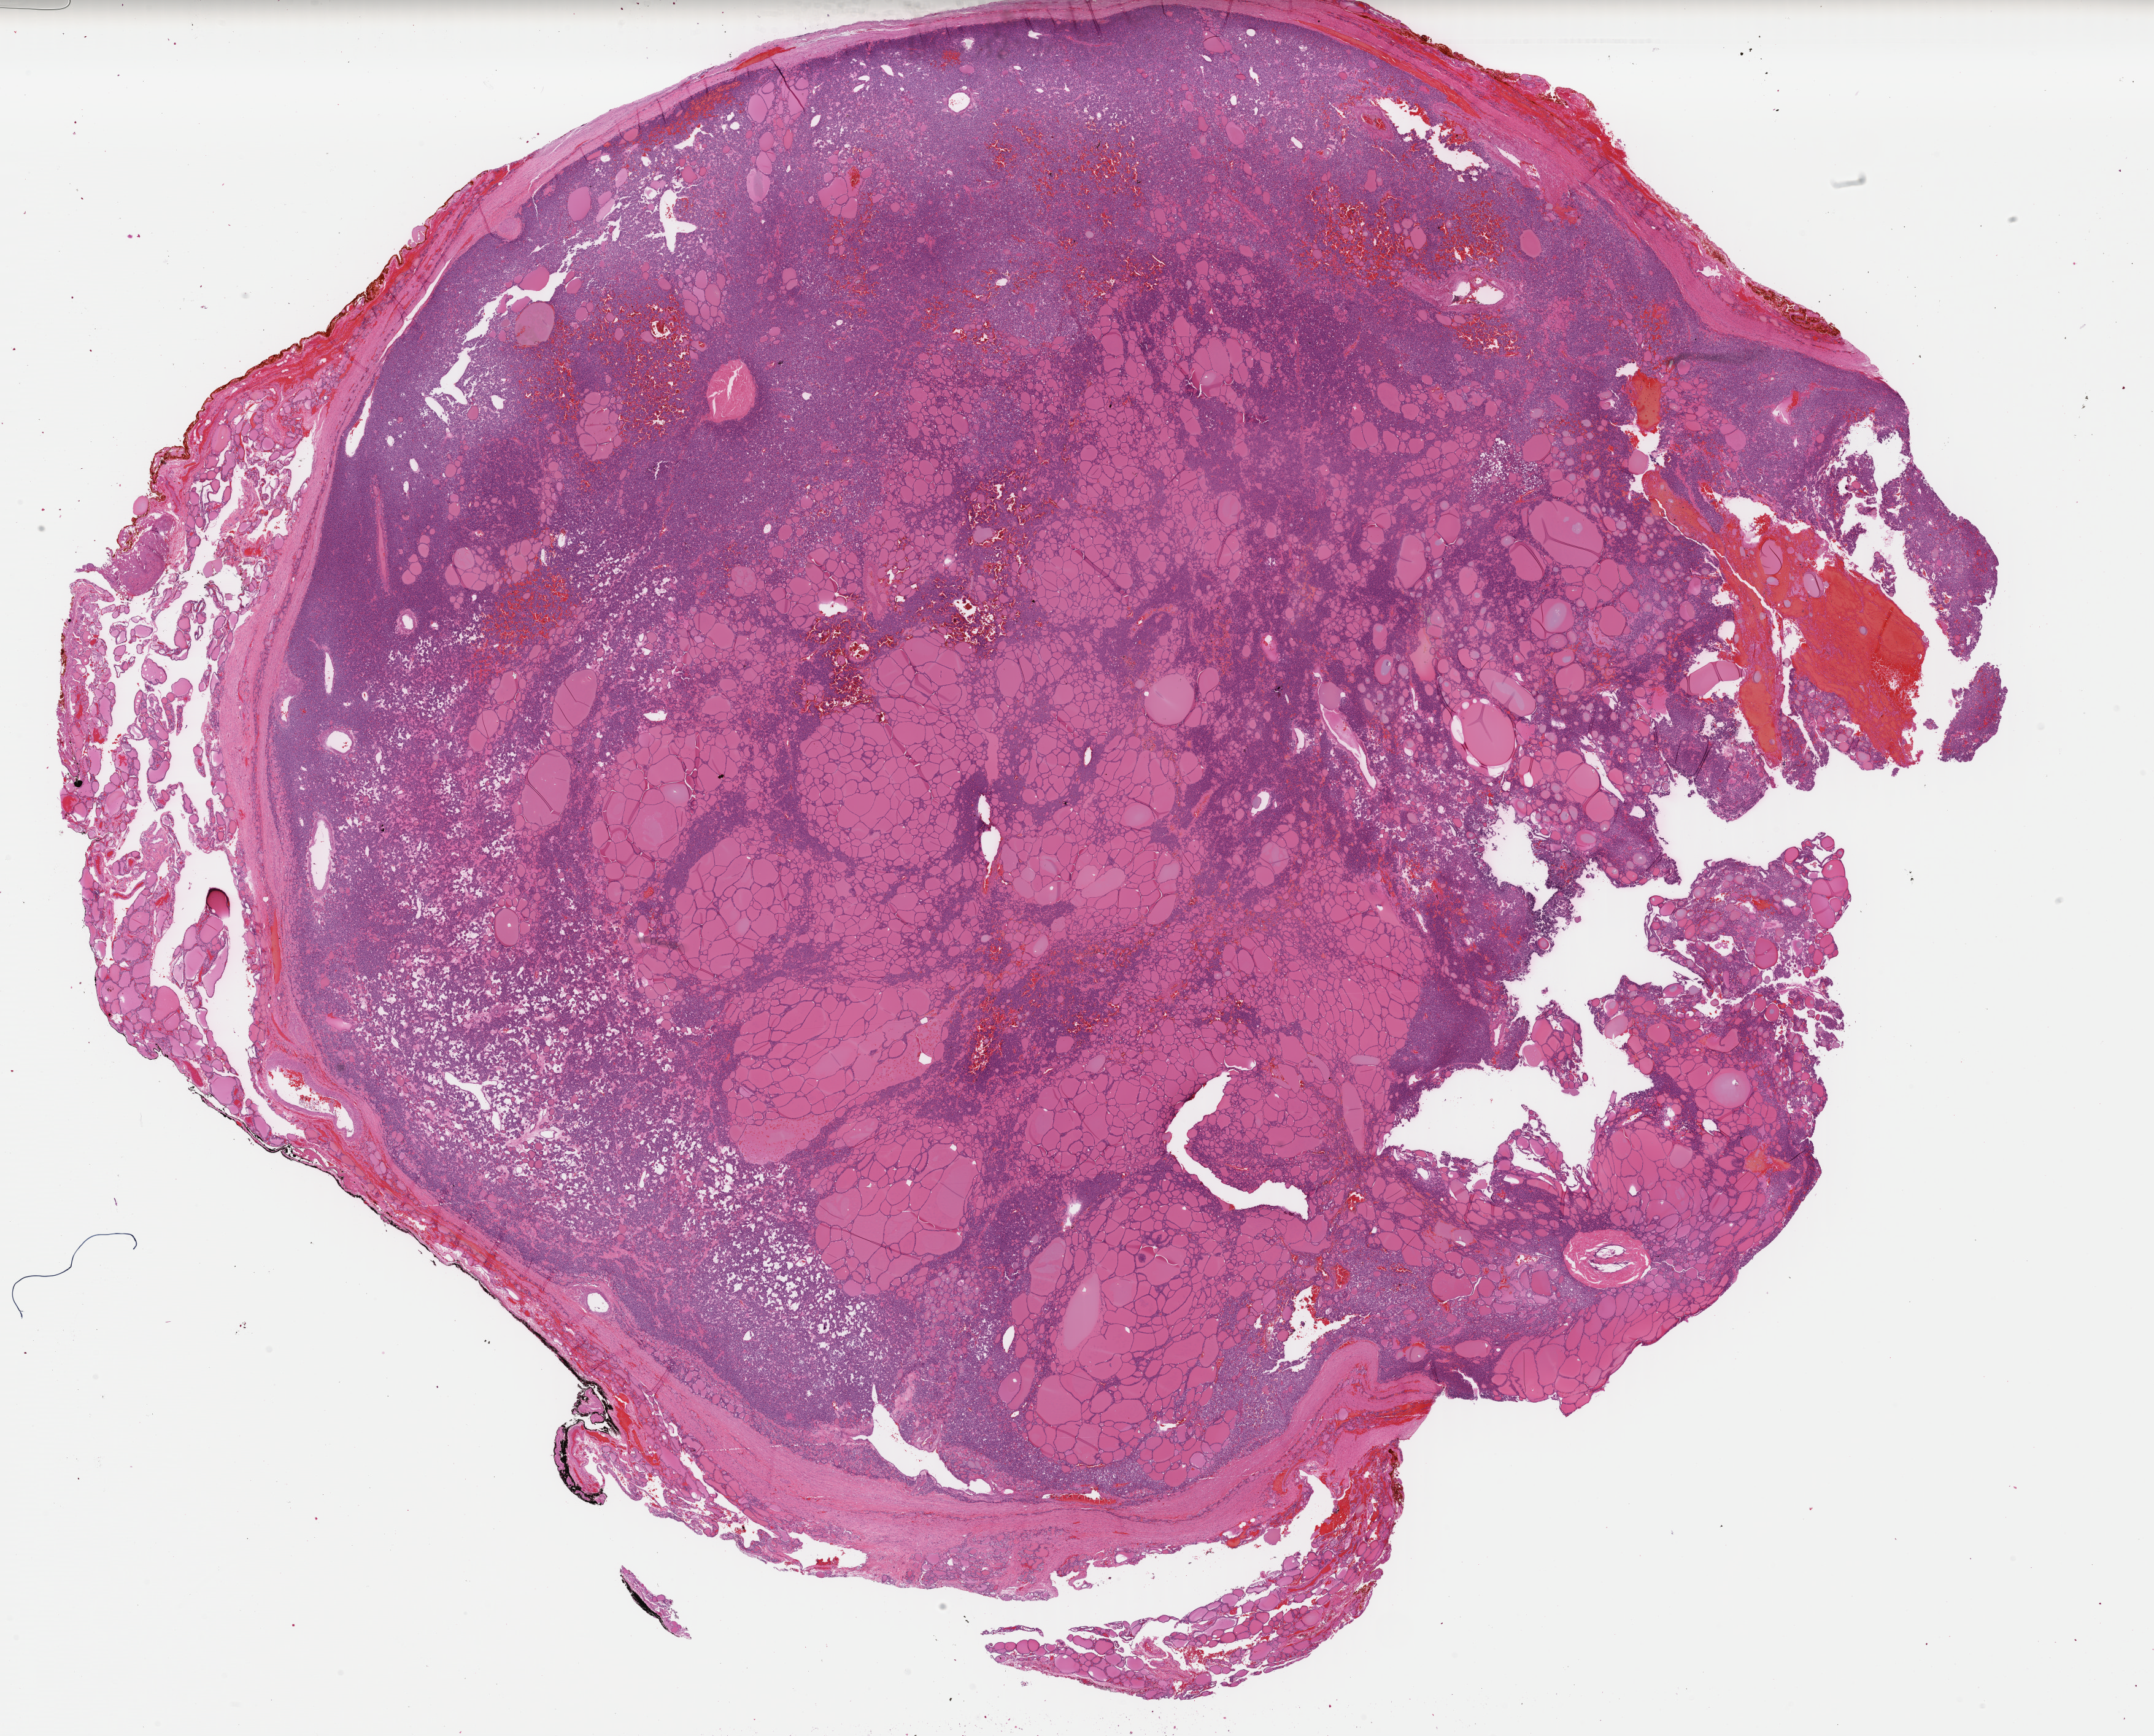
Whole-slide histology image, Hematoxylin and eosin (H&E) stained — whole scanned area (about 27.7 x 22.3 mm) shown as a low-resolution overview. Formalin-fixed paraffin-embedded (FFPE) diagnostic section. Thyroid, primary tumour sample. Female patient; age at initial diagnosis 45 years.
Diagnosis: Papillary carcinoma, follicular variant (thyroid gland). AJCC pathologic stage: II.